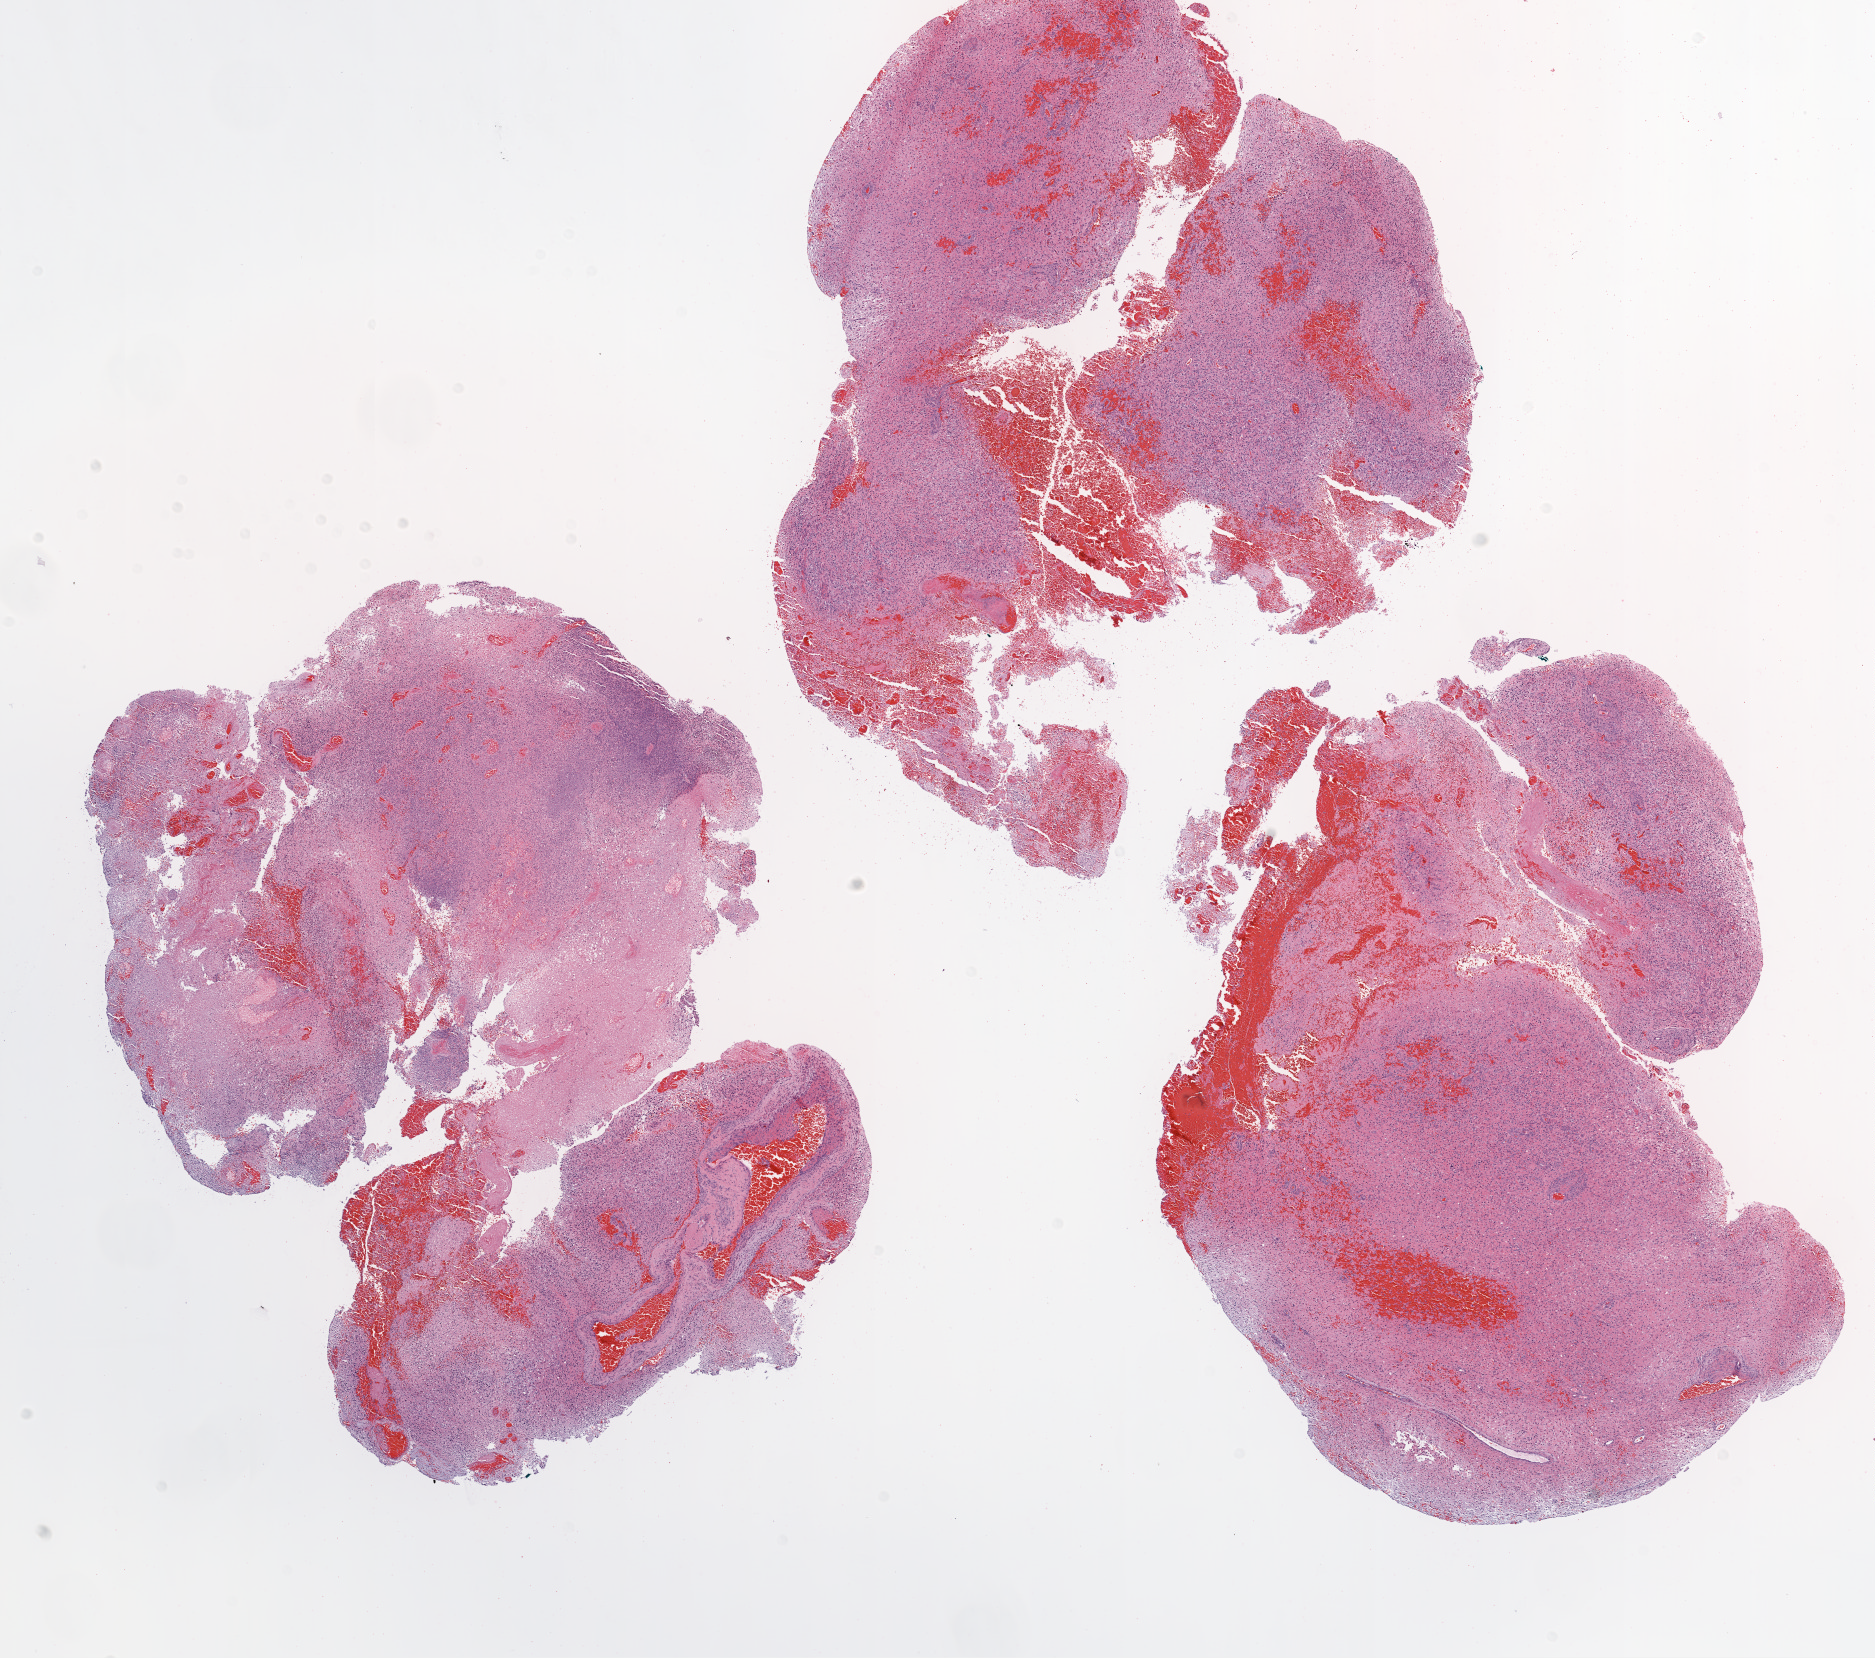
Whole-slide histology image, H&E — low-resolution overview of the scanned area, about 15.0 x 13.3 mm (acquisition: 20x scan). Formalin-fixed paraffin-embedded (FFPE) diagnostic section. Primary tumour sample from the brain. Patient: male, age at initial diagnosis 43 years.
Pathologic diagnosis: Glioblastoma.